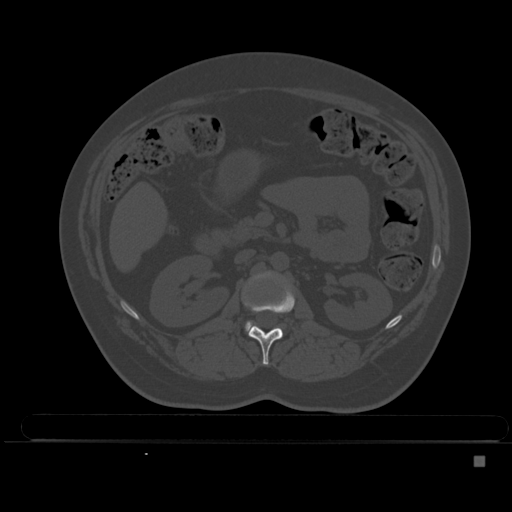
CT including the spine, one axial slice; position 187 of 495 along the scan axis; bone window (W 1800 / L 400 HU); 1.5 mm slice thickness; 512 × 512 image matrix, field of view 404 × 404 mm. Female patient, age 33 years. Case-level facts recorded for this patient, not image findings: primary cancer: breast; vertebrae with lytic lesions (as recorded): T1.
Annotated regions visible in this slice (semi-automatic segmentation, software-assisted and operator-edited):
- L1 vertebra: bounding box [x1, y1, x2, y2] px = [244, 280, 295, 365]
- L2 vertebra: [245, 321, 252, 331]